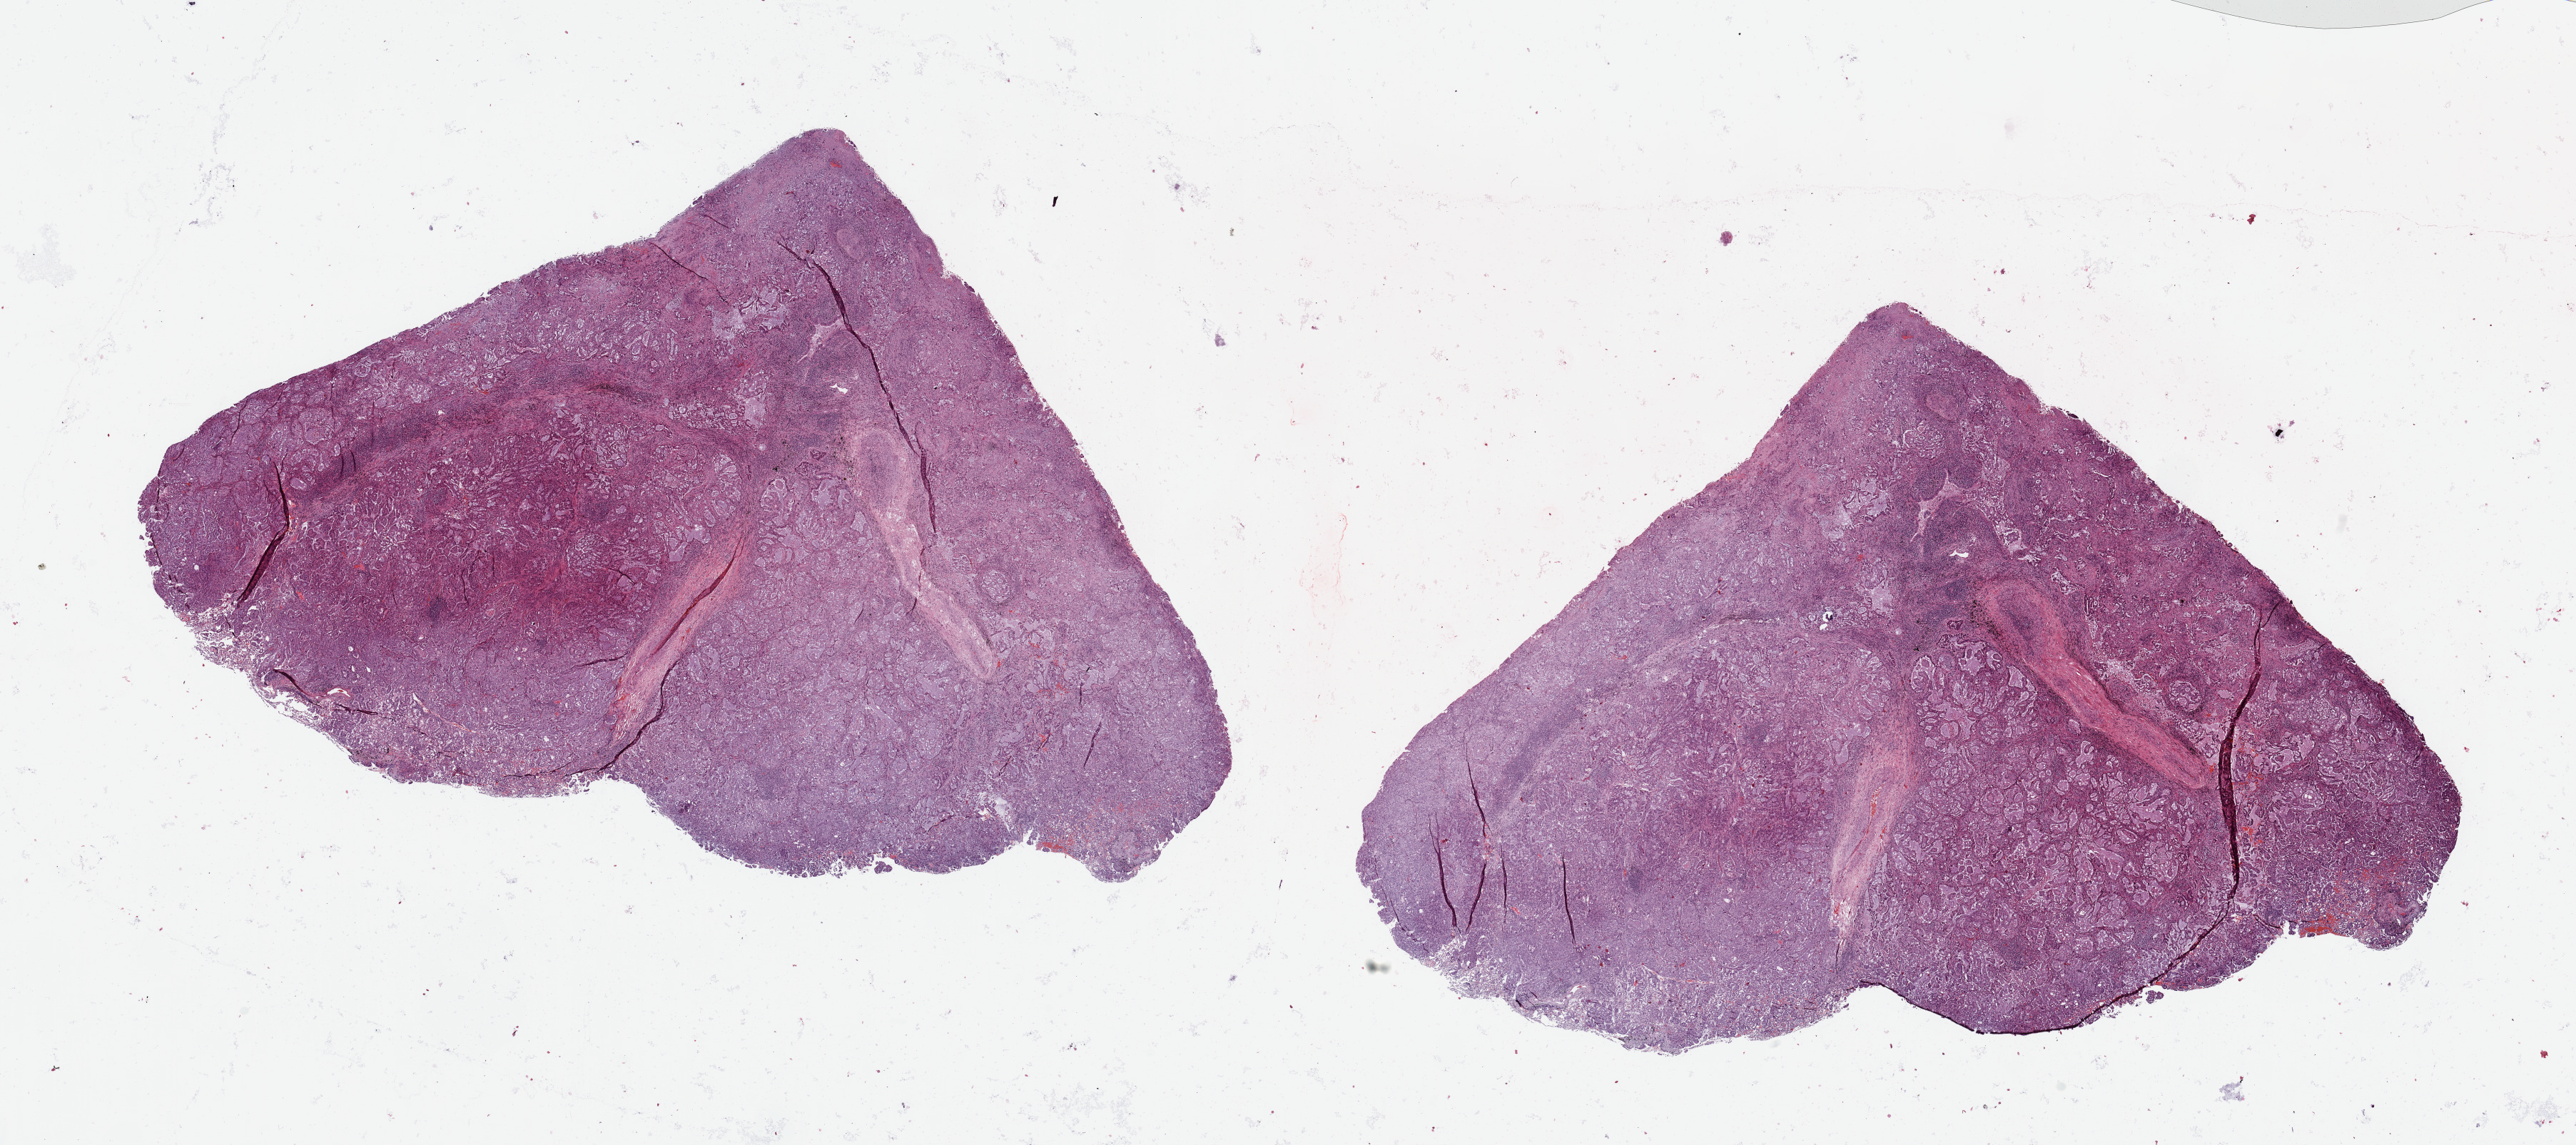
Whole-slide histology image, H&E-stained — a low-resolution overview of the entire scanned area, about 28.5 x 12.7 mm; tumour tissue sample, sampled site: lung. Patient: female, age 70 years. Histologic grade: G1 (well differentiated). Pathologist review of this section (percent, as recorded): tumour nuclei 75%, necrosis 5%.
* diagnosis: Adenocarcinoma, NOS
* AJCC pathologic stage: IIIA